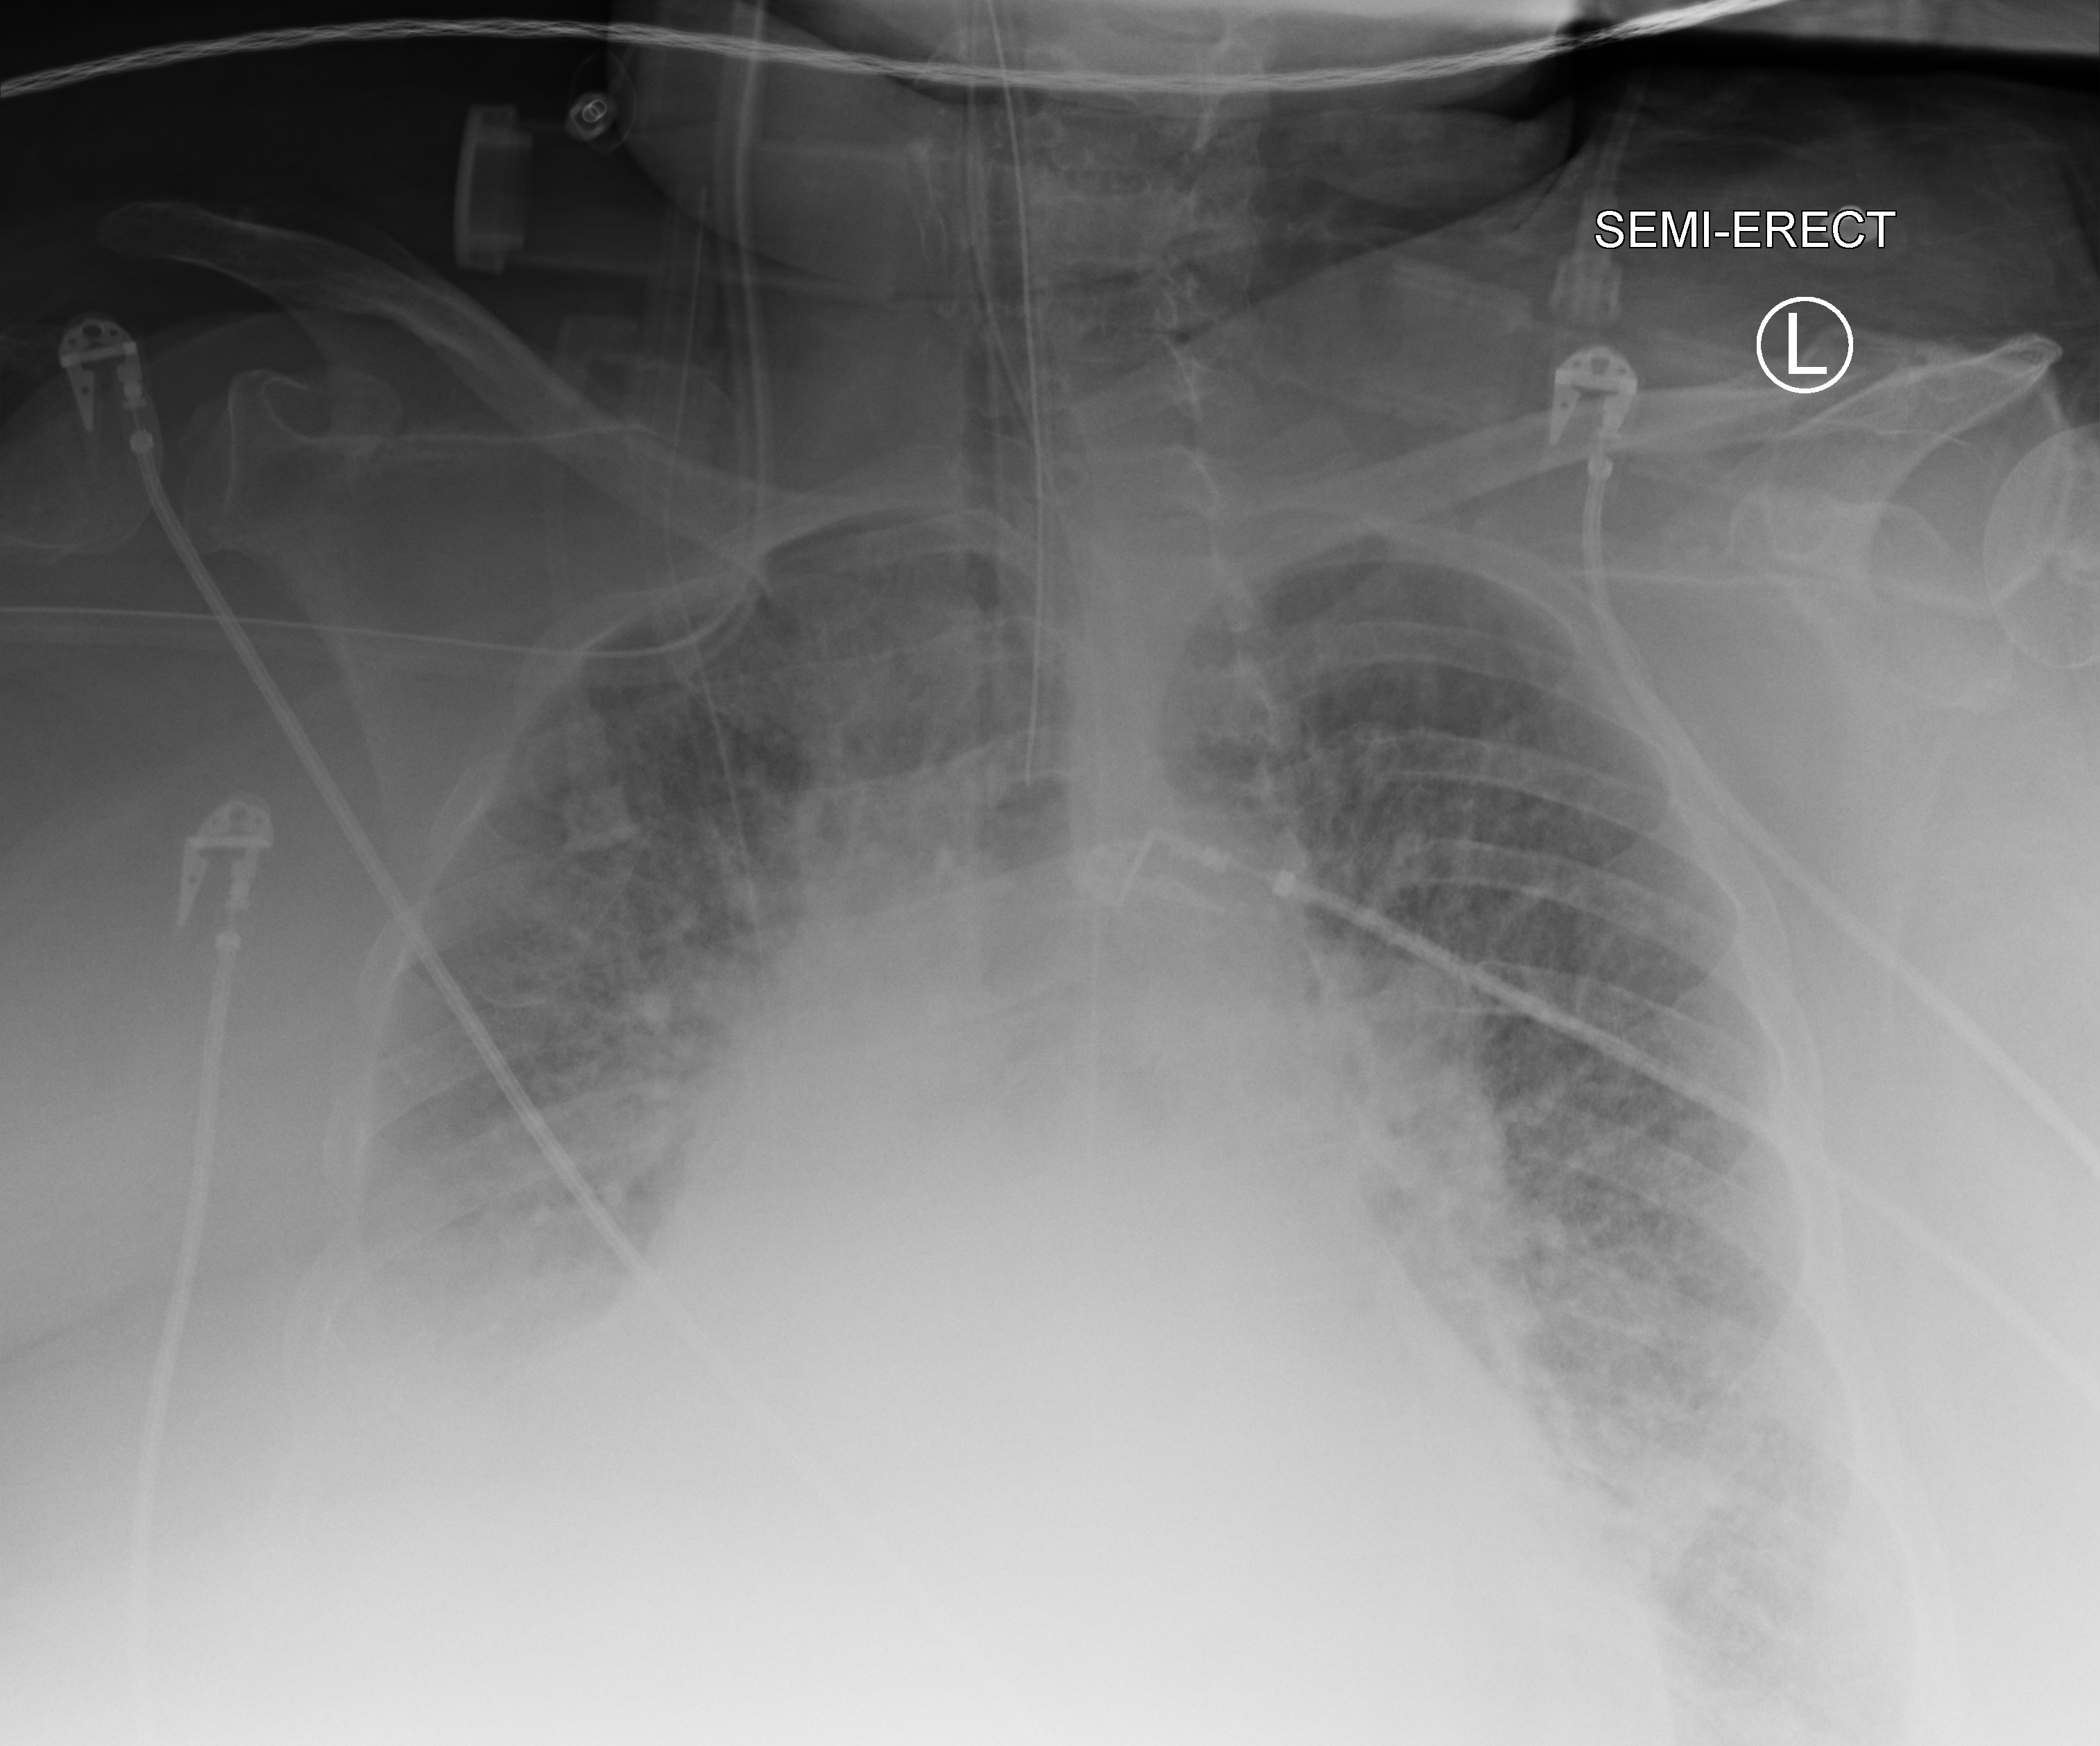
Chest X-ray (portable), anteroposterior (AP) projection. Female patient hospitalised with COVID-19, age 60–74 years.
From the hospital-stay record, not from the radiograph (when in the stay this image was taken is not recorded):
- admitted to intensive care during this hospital stay: yes
- mechanically ventilated during this hospital stay: yes
- length of hospital stay: 6 days